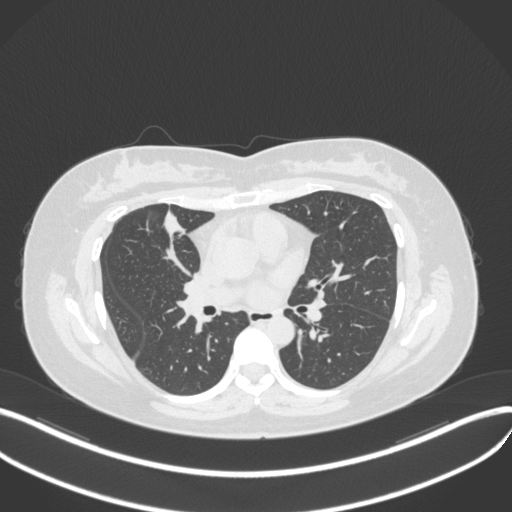
Chest CT, one axial slice; slice 168 of 272 in the series (ordered by position); reconstruction kernel B31f; 120 kVp; lung window (W 1500 / L -600 HU); 512 × 512 image matrix, field of view 400 × 400 mm. Patient: female, 42 years. Case-level facts recorded for this patient, not image findings: clinical TNM (as recorded): T1b N0 M0.
Annotated regions visible in this slice (rectangle marked by the reading radiologist):
- lung tumour (recorded histology: adenocarcinoma): bounding box (x1, y1, x2, y2) in pixels: (155, 206, 192, 246)